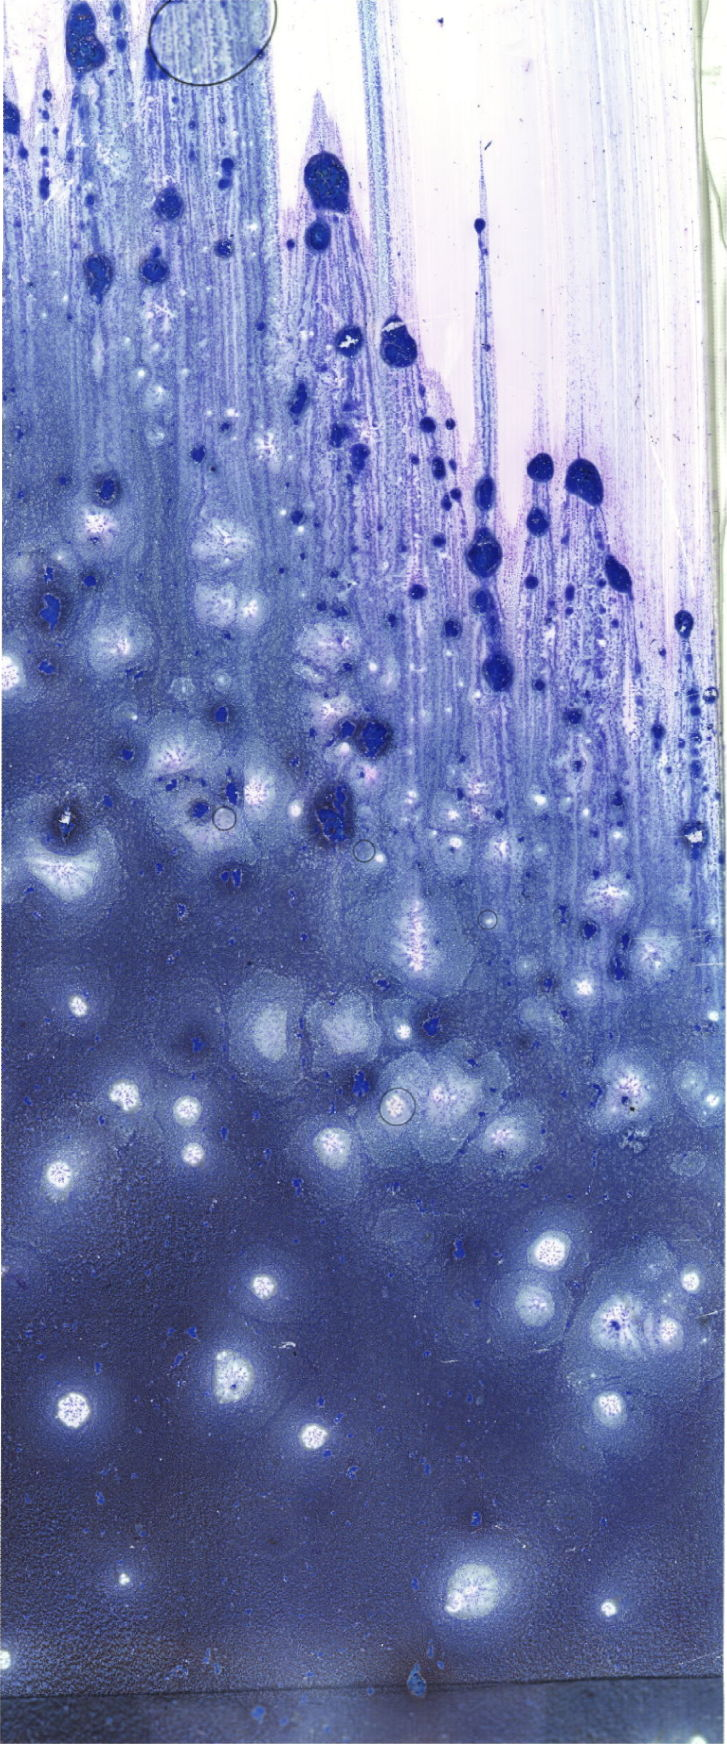
Bone marrow aspirate smear, May-Grünwald–Giemsa stain, whole-slide image — a low-resolution overview of the entire scanned area, about 20.6 x 49.4 mm.
Diagnosis: Acute Myeloid Leukemia without Maturation.